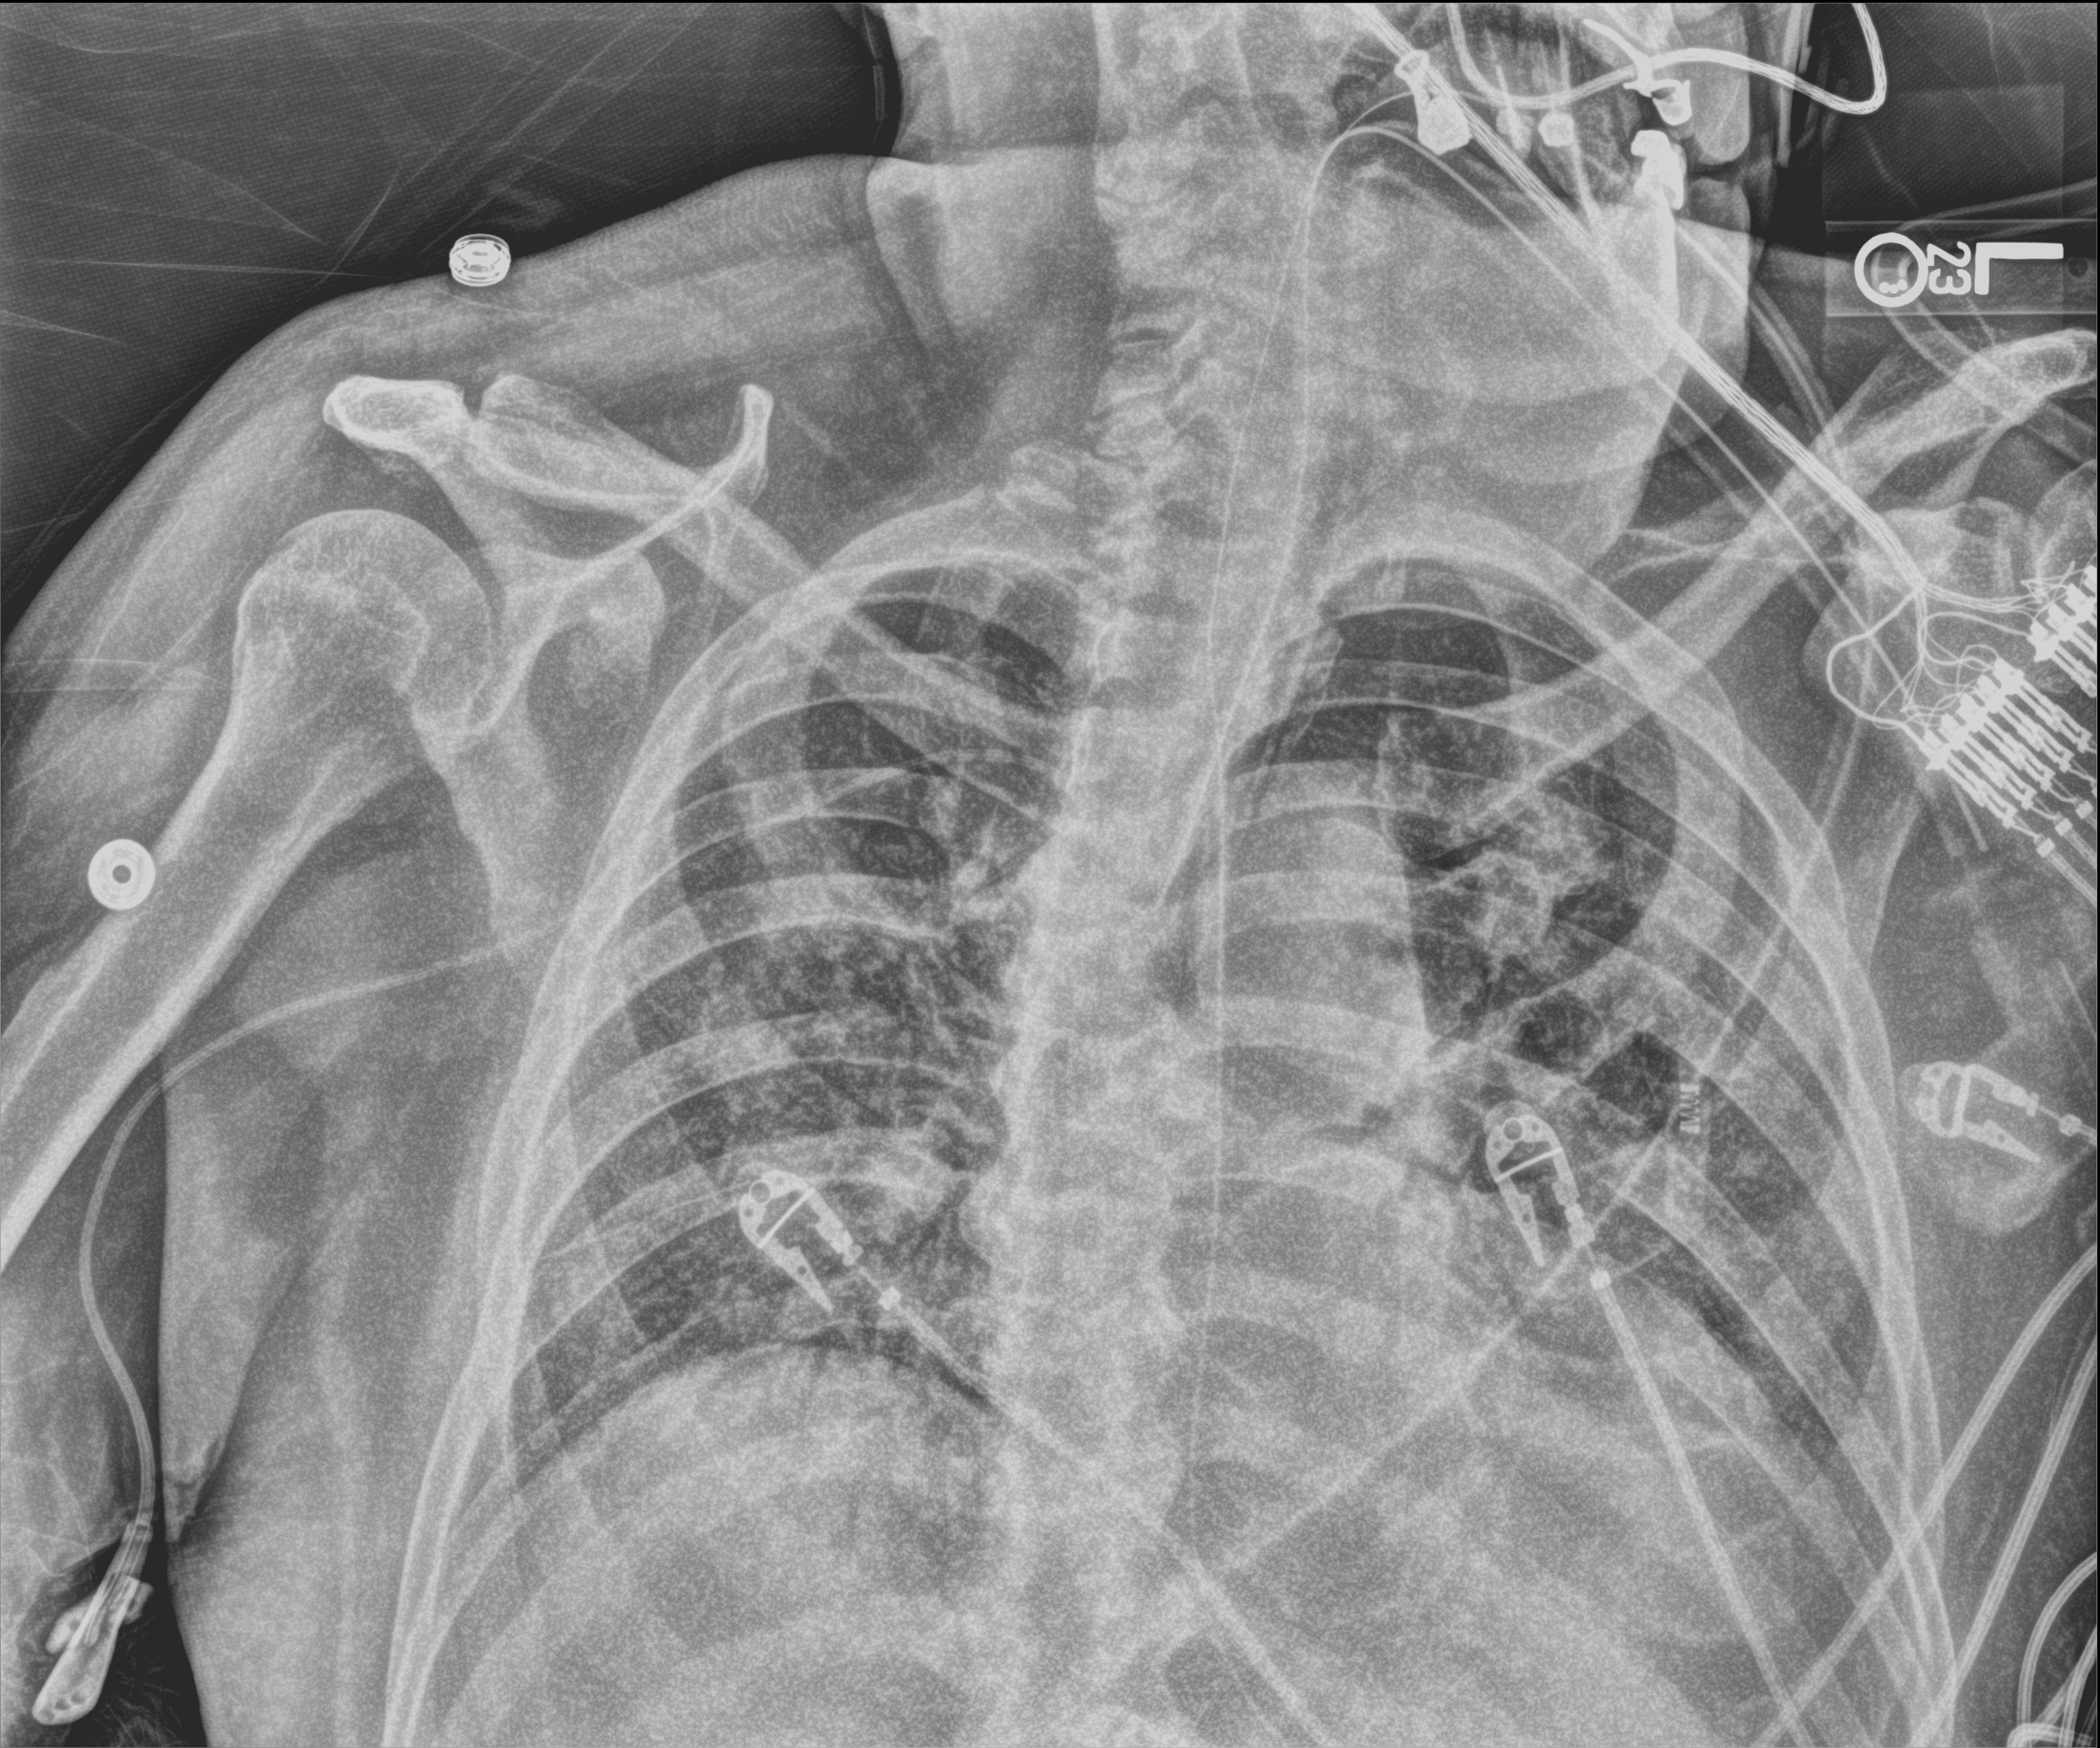
Bedside chest radiograph (computed radiography); anteroposterior (AP) projection. Patient hospitalised with COVID-19; male, aged 75–90 years.
Admission-level facts for this patient (not findings on this image; timing relative to this image not recorded):
- mechanically ventilated during this hospital stay: yes